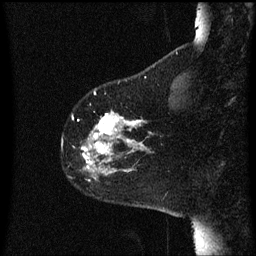
Breast MRI (dynamic contrast-enhanced), one sagittal slice. Dynamic contrast-enhanced series, image 2 of 3 at this slice position (ordered by acquisition). 1.5 T. TE 4.2 ms, TR 8 ms. 2 mm slice thickness. 256 × 256 image matrix. Female patient, age 60 years.
Structures marked on this image (semi-automatic segmentation, software-assisted and operator-edited):
- analysis volume of interest (the breast-tissue region the enhancement analysis was run in; not a lesion): bounding box (x1, y1, x2, y2) in pixels: (79, 110, 152, 181)
- tumour enhancement mask (voxels above the 70 % enhancement threshold inside the analysis volume of interest): (82, 112, 139, 169)